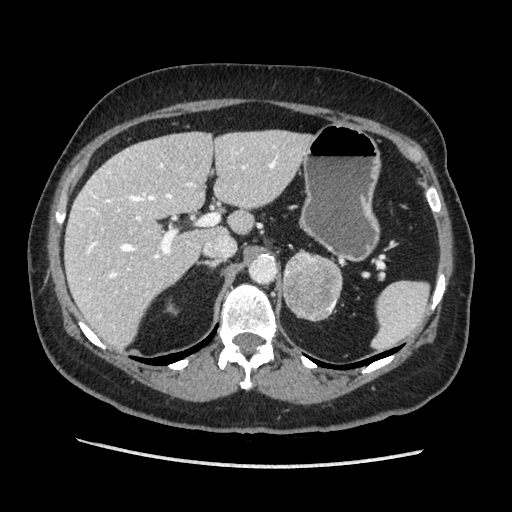
Contrast-enhanced abdominal CT, one axial slice. Slice 128 of 203 in the series (ordered by position). Soft-tissue window (W 400 / L 40 HU). 512 × 512 image matrix. Female patient. From the clinical record (not read from this slice): diagnosis: adrenocortical carcinoma; tumour side: left adrenal; tumour size at pathology: 6.5 cm; Ki-67 index: 22 %; stage (as recorded): 2.
Annotated regions visible in this slice (semi-automatically segmented with operator editing):
- mass: box from (x=283, y=250) to (x=343, y=320) px